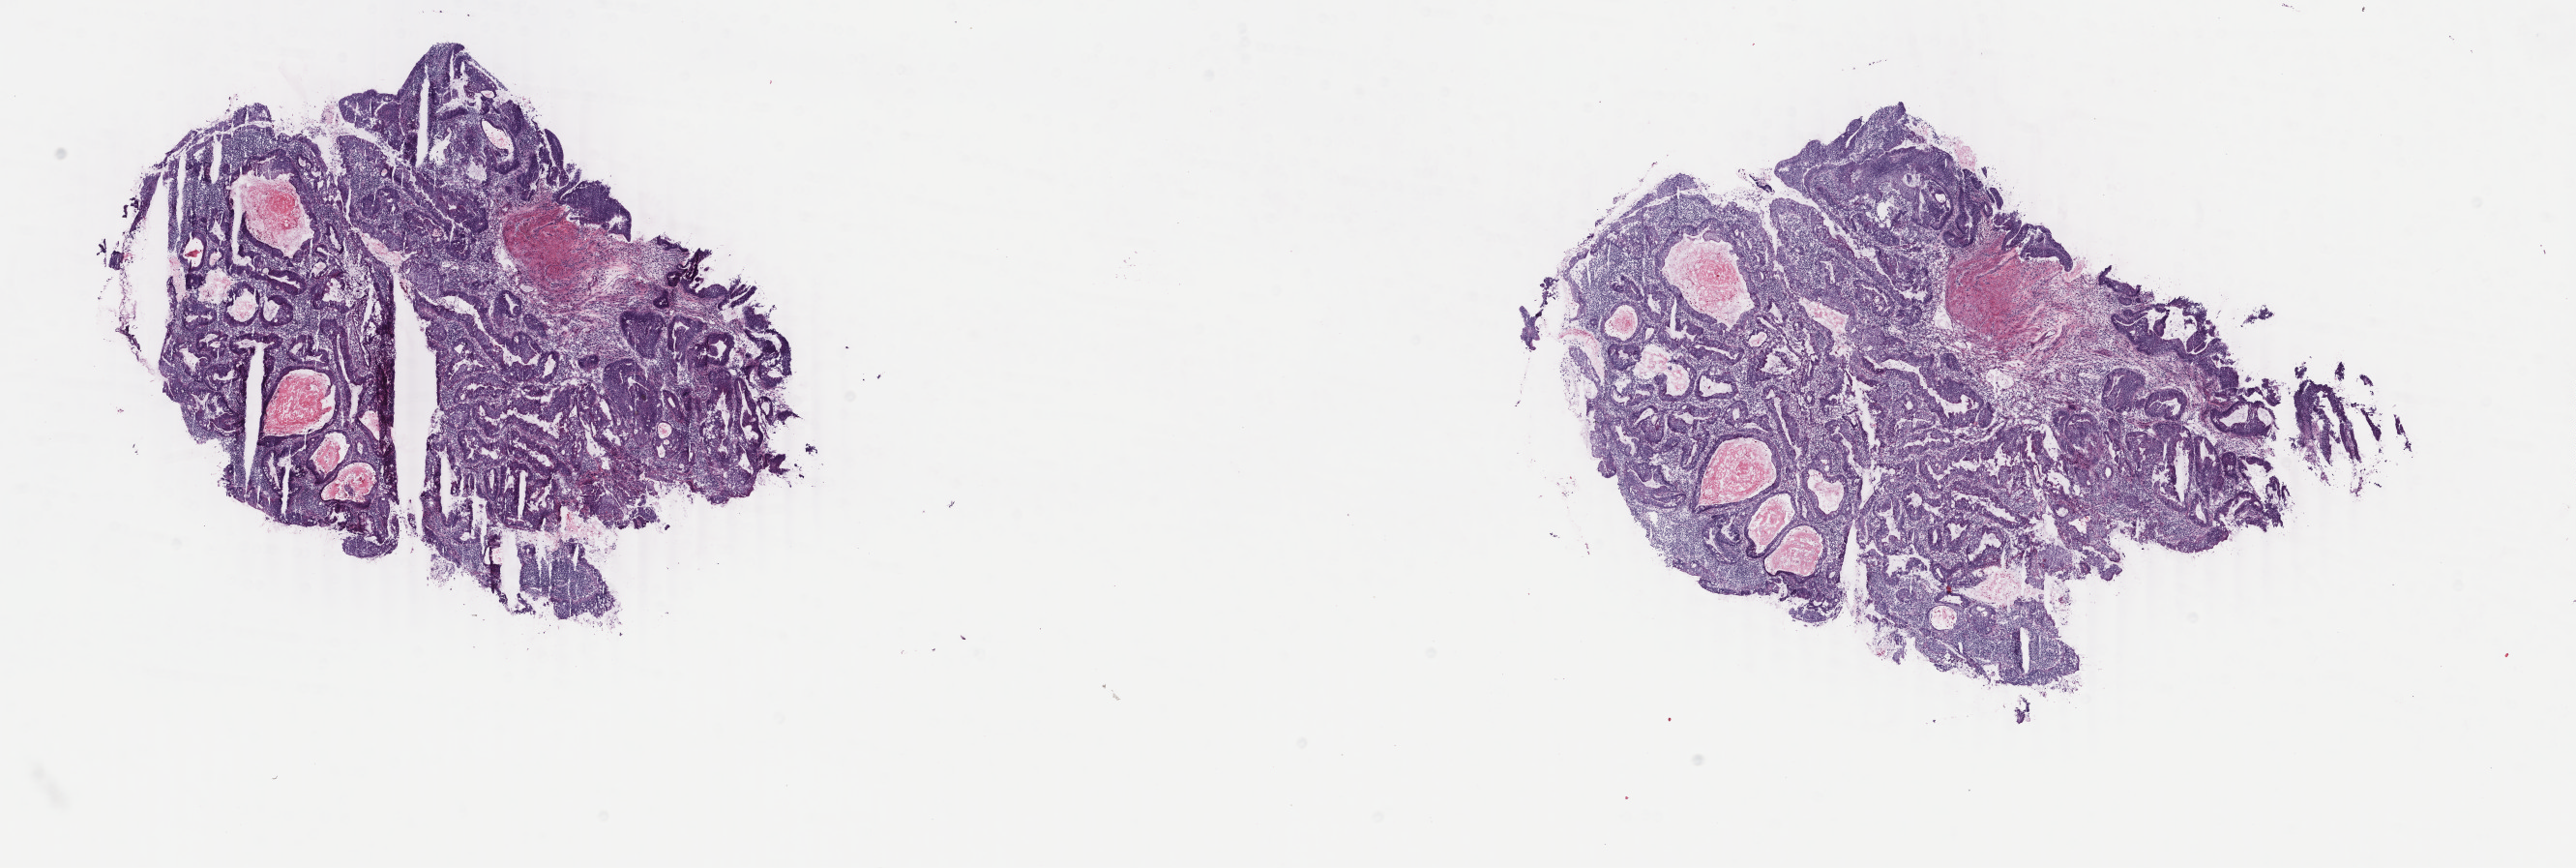
H&E whole-slide image — low-resolution overview of the scanned area, about 21.2 x 7.1 mm (from a 40x scan); frozen section from the bottom of the tissue portion; sample: primary tumour, colon. Male patient; age at initial diagnosis 59 years. Pathologist review of this section (percent, as recorded): tumour cells 60%, tumour nuclei 60%, normal cells 0%, stromal cells 35%, necrosis 5%. Inflammatory infiltration, as recorded: lymphocyte infiltration 8%, monocyte infiltration 3%, neutrophil infiltration 12%.
* AJCC pathologic stage: I (5th edition)
* pathologic diagnosis: Adenocarcinoma, NOS